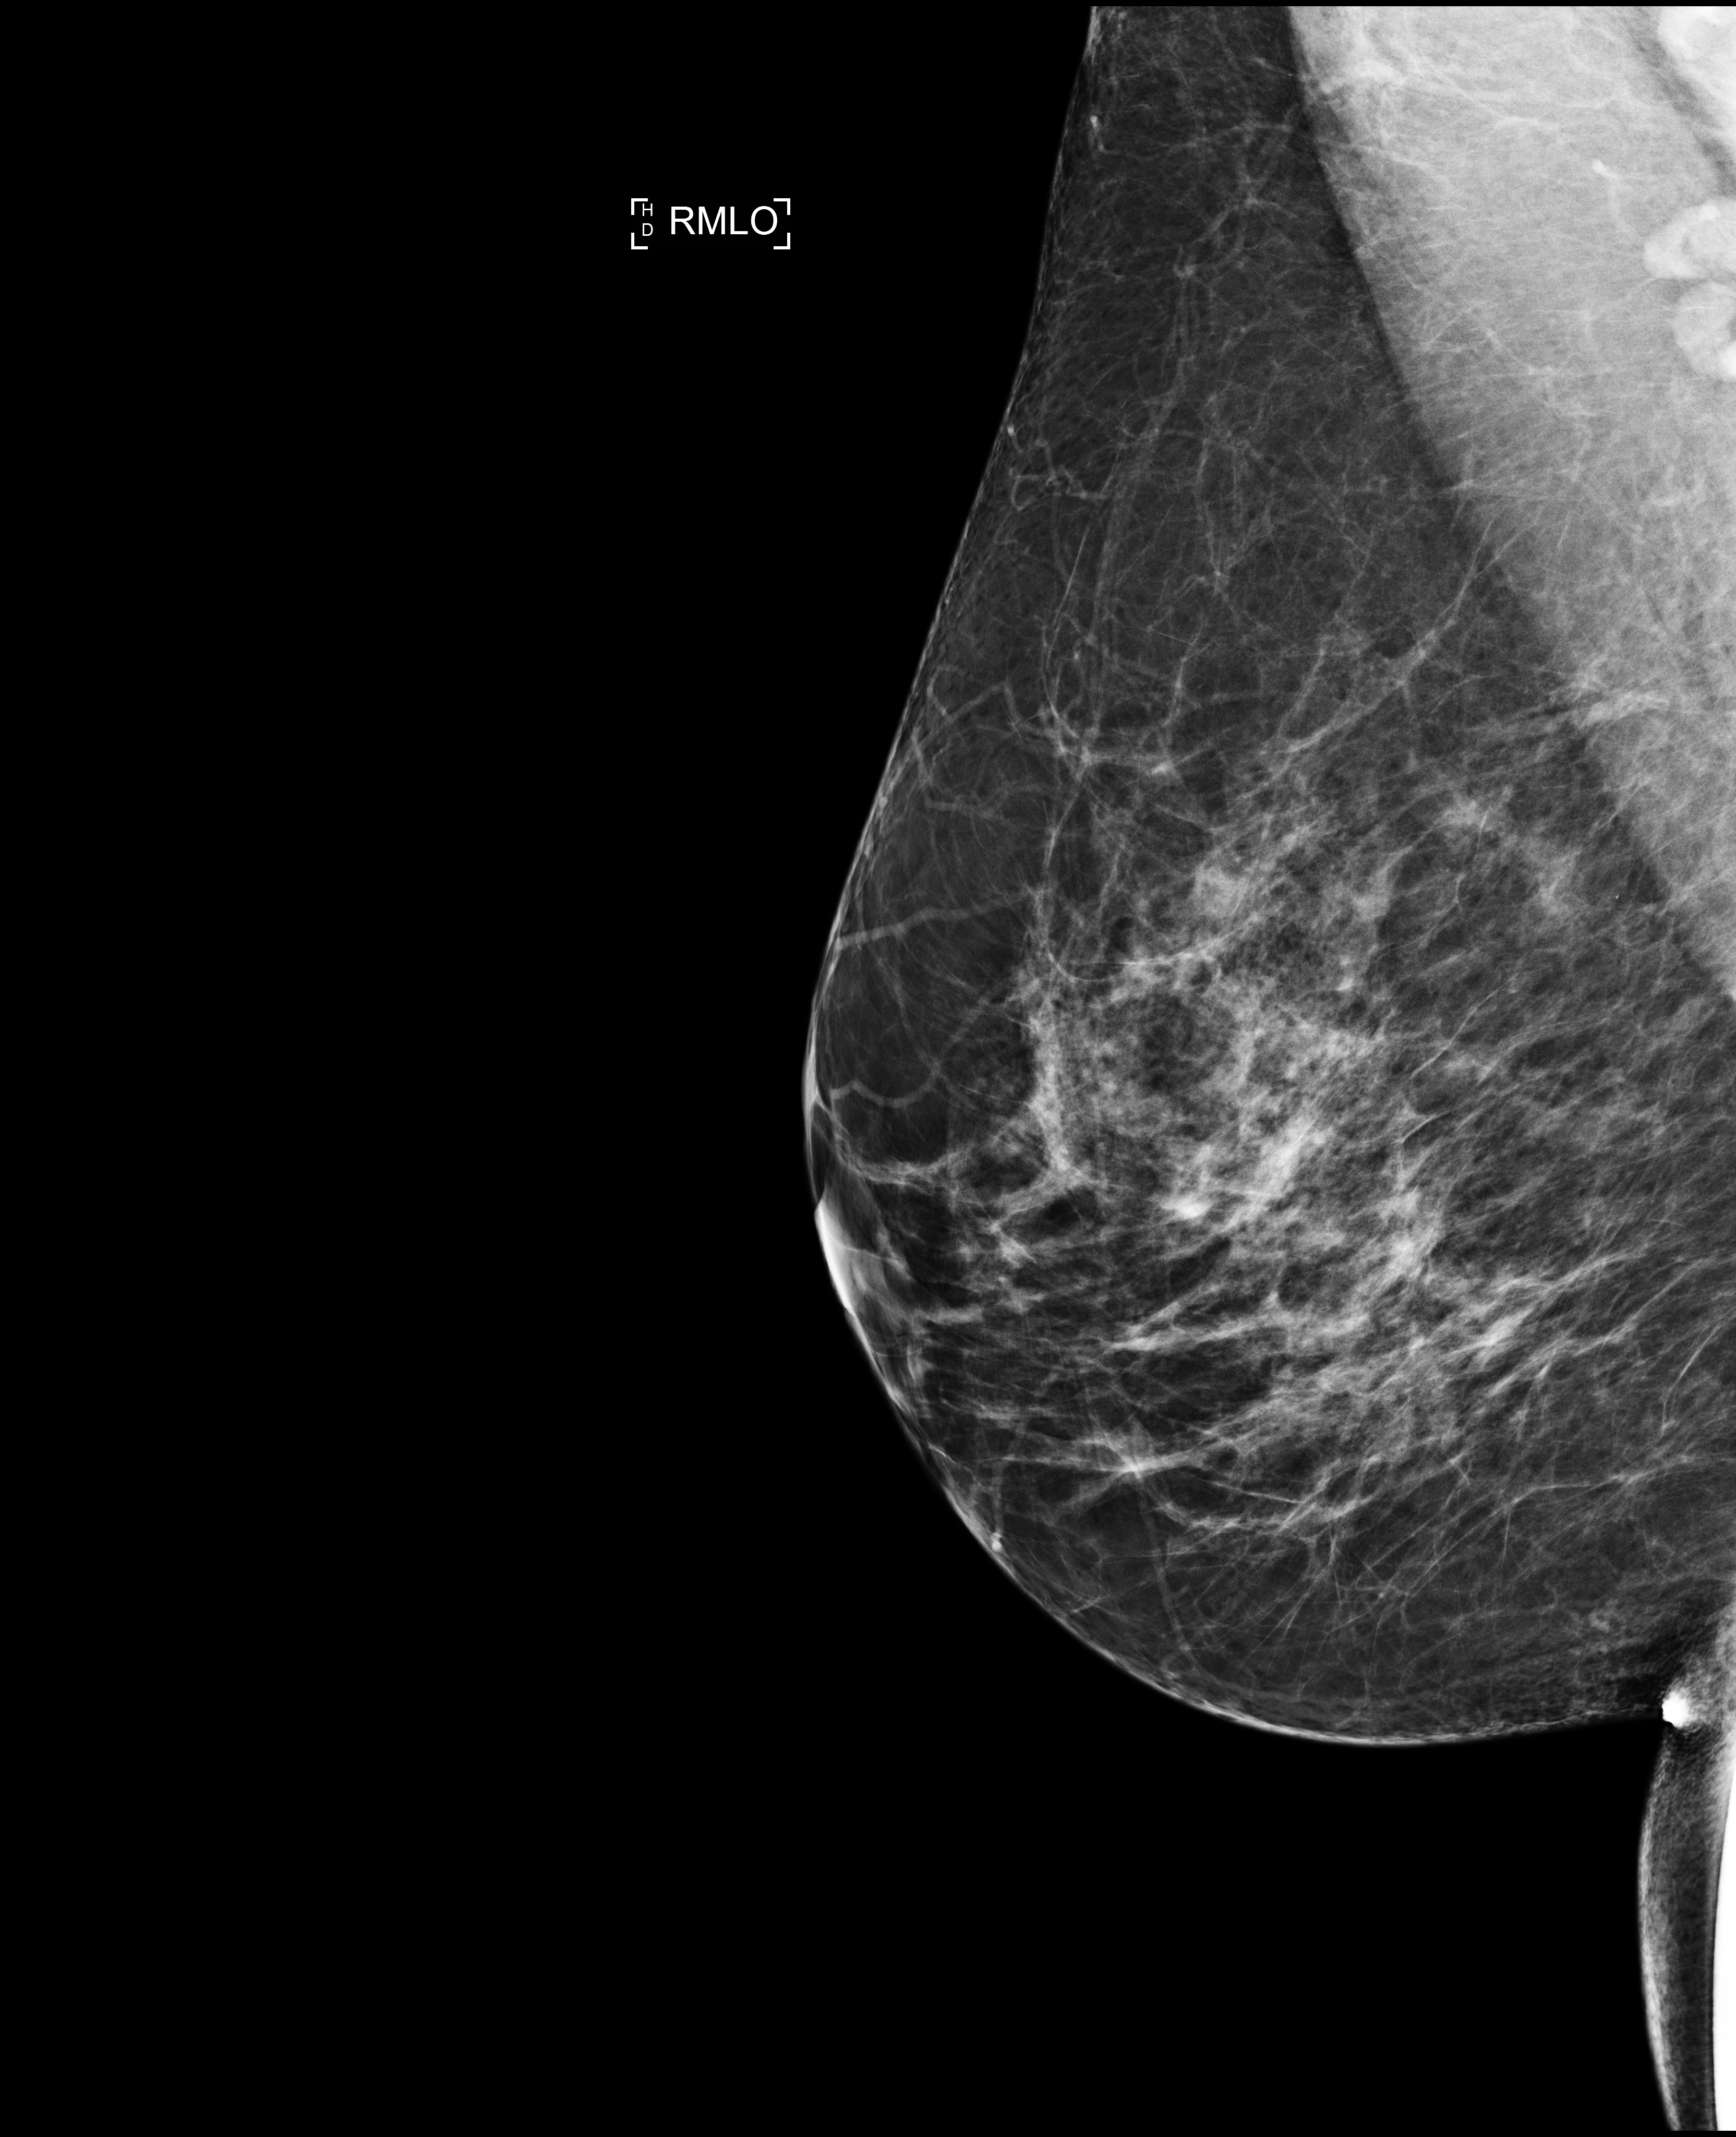
Screening examination. Patient: female, 51 years.
Image type: full-field digital mammogram. Breast: right. Projection: mediolateral oblique (MLO) view.